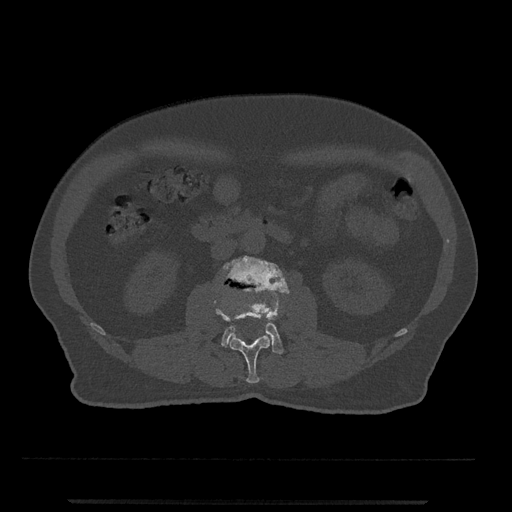
CT including the spine, one axial slice; slice 239 of 797 in the series (ordered by position); reconstruction kernel Br40s/3; bone window (W 1800 / L 400 HU); 512 × 512 image matrix, field of view 419 × 419 mm. Patient: male, 63 years. Case-level facts recorded for this patient, not image findings: primary cancer: prostate.
Outlined on this slice (semi-automatically segmented with operator editing):
- L2 vertebra: bounding box (x1, y1, x2, y2) in pixels: (214, 291, 278, 383)
- L3 vertebra: (220, 256, 289, 354)